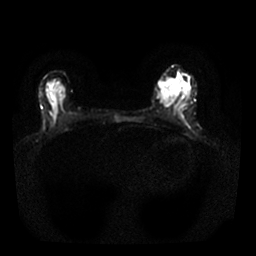
Breast MRI, one axial slice; position 10 of 25 along the scan axis; diffusion-weighted series; image 2 of 4 stored at this slice position (different b-values; order by instance number); 1.5 T; 4 mm slice thickness; 256 × 256 image matrix. Female patient.
Outlined on this slice (outlined manually by an expert reader):
- tumour on diffusion-weighted imaging: bounding box (x1, y1, x2, y2) in pixels: (158, 80, 178, 107)